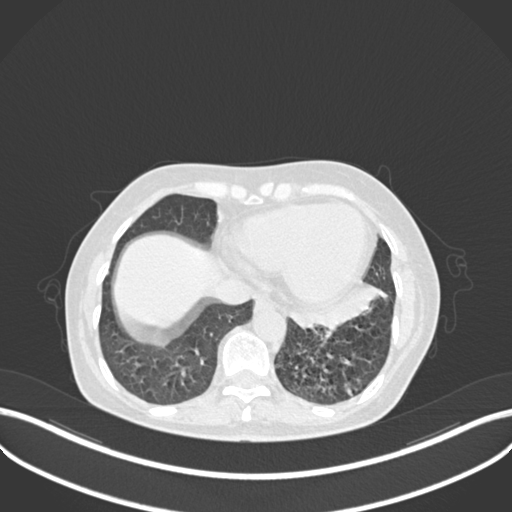
Chest CT, one axial slice. Slice 71 of 270 in the series (ordered by position). Reconstruction kernel B30f. 120 kVp. Lung window (W 1500 / L -600 HU). 1 mm slice thickness. 512 × 512 image matrix, field of view 400 × 400 mm. Female patient, age 63 years. Case-level facts recorded for this patient, not image findings: clinical TNM (as recorded): T1b N0 M0.
Structures marked on this image (bounding box drawn by a radiologist):
- lung tumour (recorded histology: adenocarcinoma): bounding box <288,274,390,339> (left, top, right, bottom; pixels)